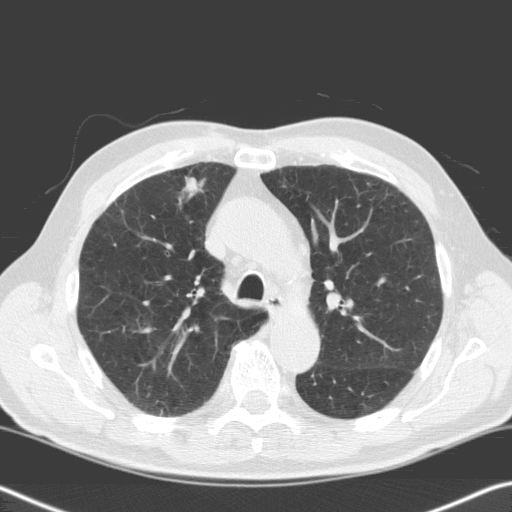
Chest CT (low-dose screening protocol), one axial image. Baseline annual screen. Lung window (W 1500 / L -600 HU). Standard (soft-tissue) reconstruction kernel (C). Slice 49 of 170 in the series. Male, age 68 years at enrolment.
- Lesion marked by an expert reader, bounding box (x1, y1, x2, y2) in pixels: (167, 168, 214, 216).
- Screening reader's record for this exam (one nodule recorded; not confirmed to be the boxed lesion): non-calcified nodule or mass ≥4 mm, right upper lobe, 18 × 12 mm, spiculated (stellate) margins, soft tissue attenuation.
- Official screen result: positive, change unspecified: nodule(s) >= 4 mm or enlarging nodule(s), mass(es), or other non-specific abnormalities suspicious for lung cancer.